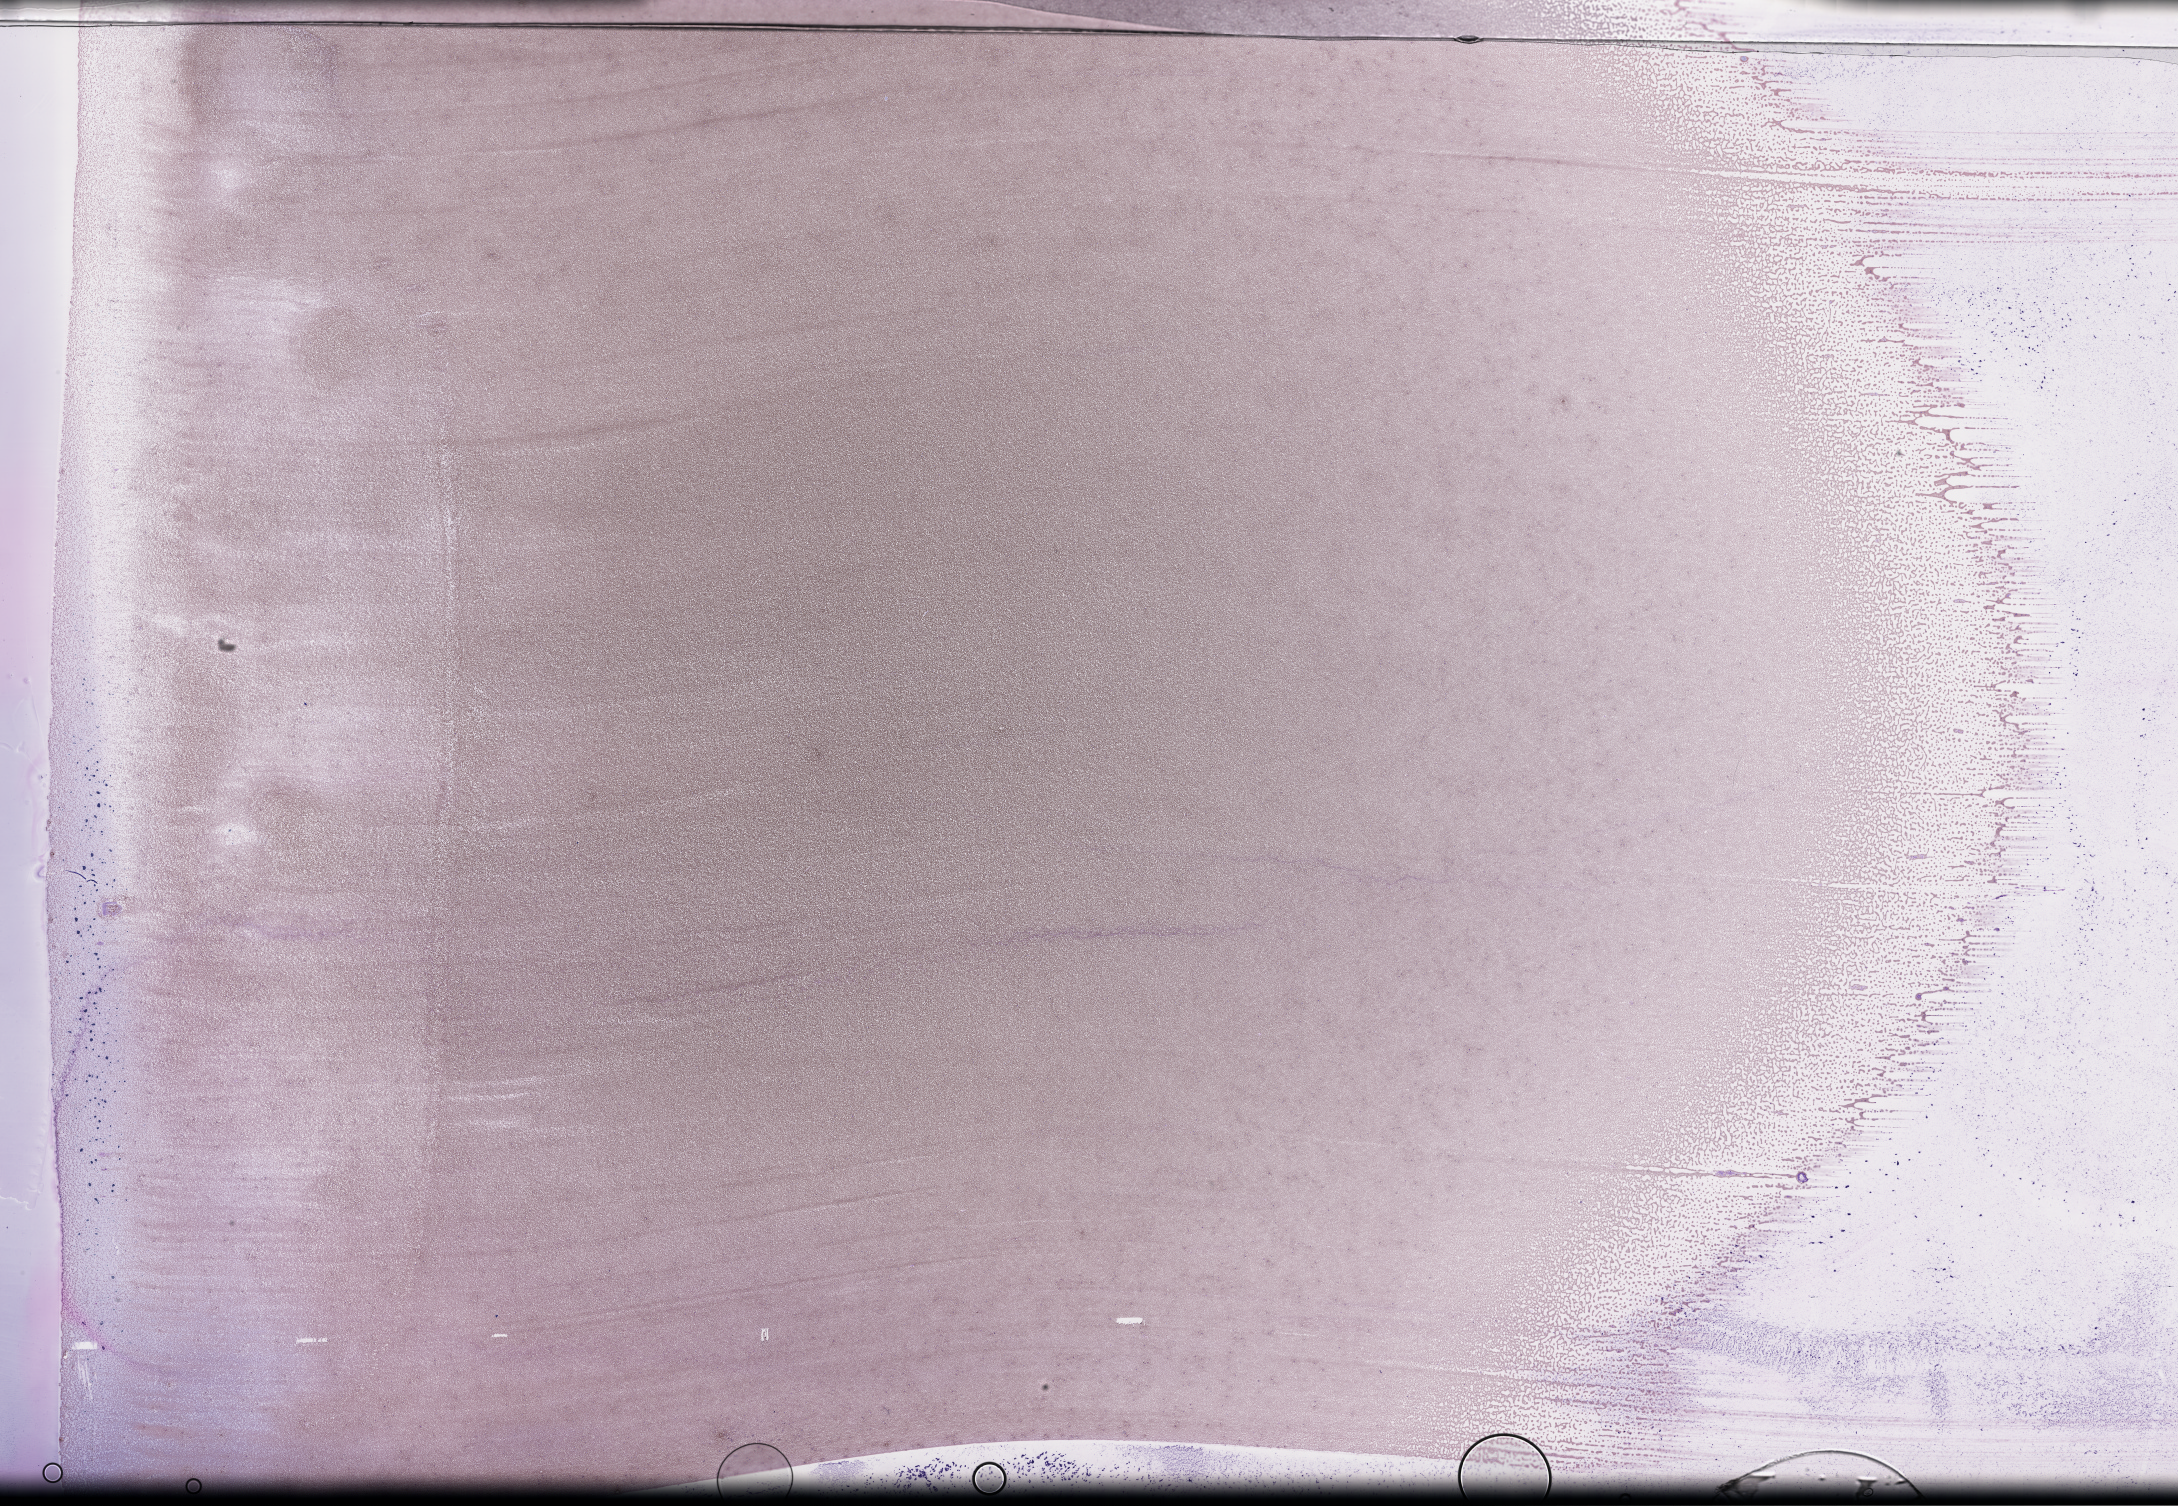
Whole-slide image of a whole blood smear, Wright-Giemsa stain — whole scanned area (about 35.2 x 24.3 mm) shown as a low-resolution overview; EDTA-anticoagulated smear; collected on treatment. Male patient.
* patient diagnosis: Plasma Cell Myeloma